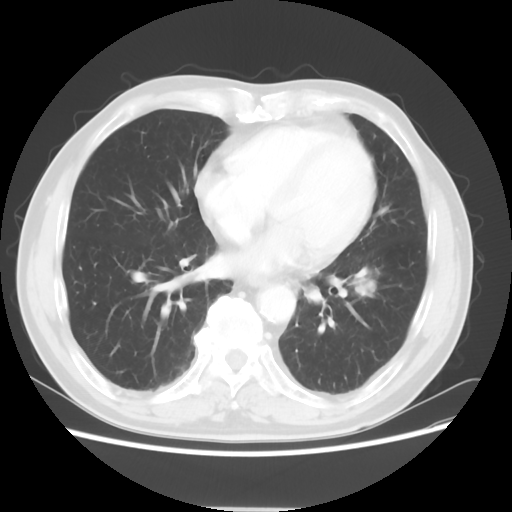
Chest CT, one axial slice. Slice 22 of 64 in the series (ordered by position). Reconstruction kernel STANDARD. Lung window (W 1500 / L -600 HU). 5 mm slice thickness. 512 × 512 image matrix, field of view 366 × 366 mm. Patient: male, 71 years. Case-level facts recorded for this patient, not image findings: clinical TNM (as recorded): T1c N1 M0; histopathological grade: G2-3.
Structures marked on this image (bounding box drawn by a radiologist):
- lung tumour (recorded histology: adenocarcinoma): bounding box [x1, y1, x2, y2] px = [342, 253, 387, 309]